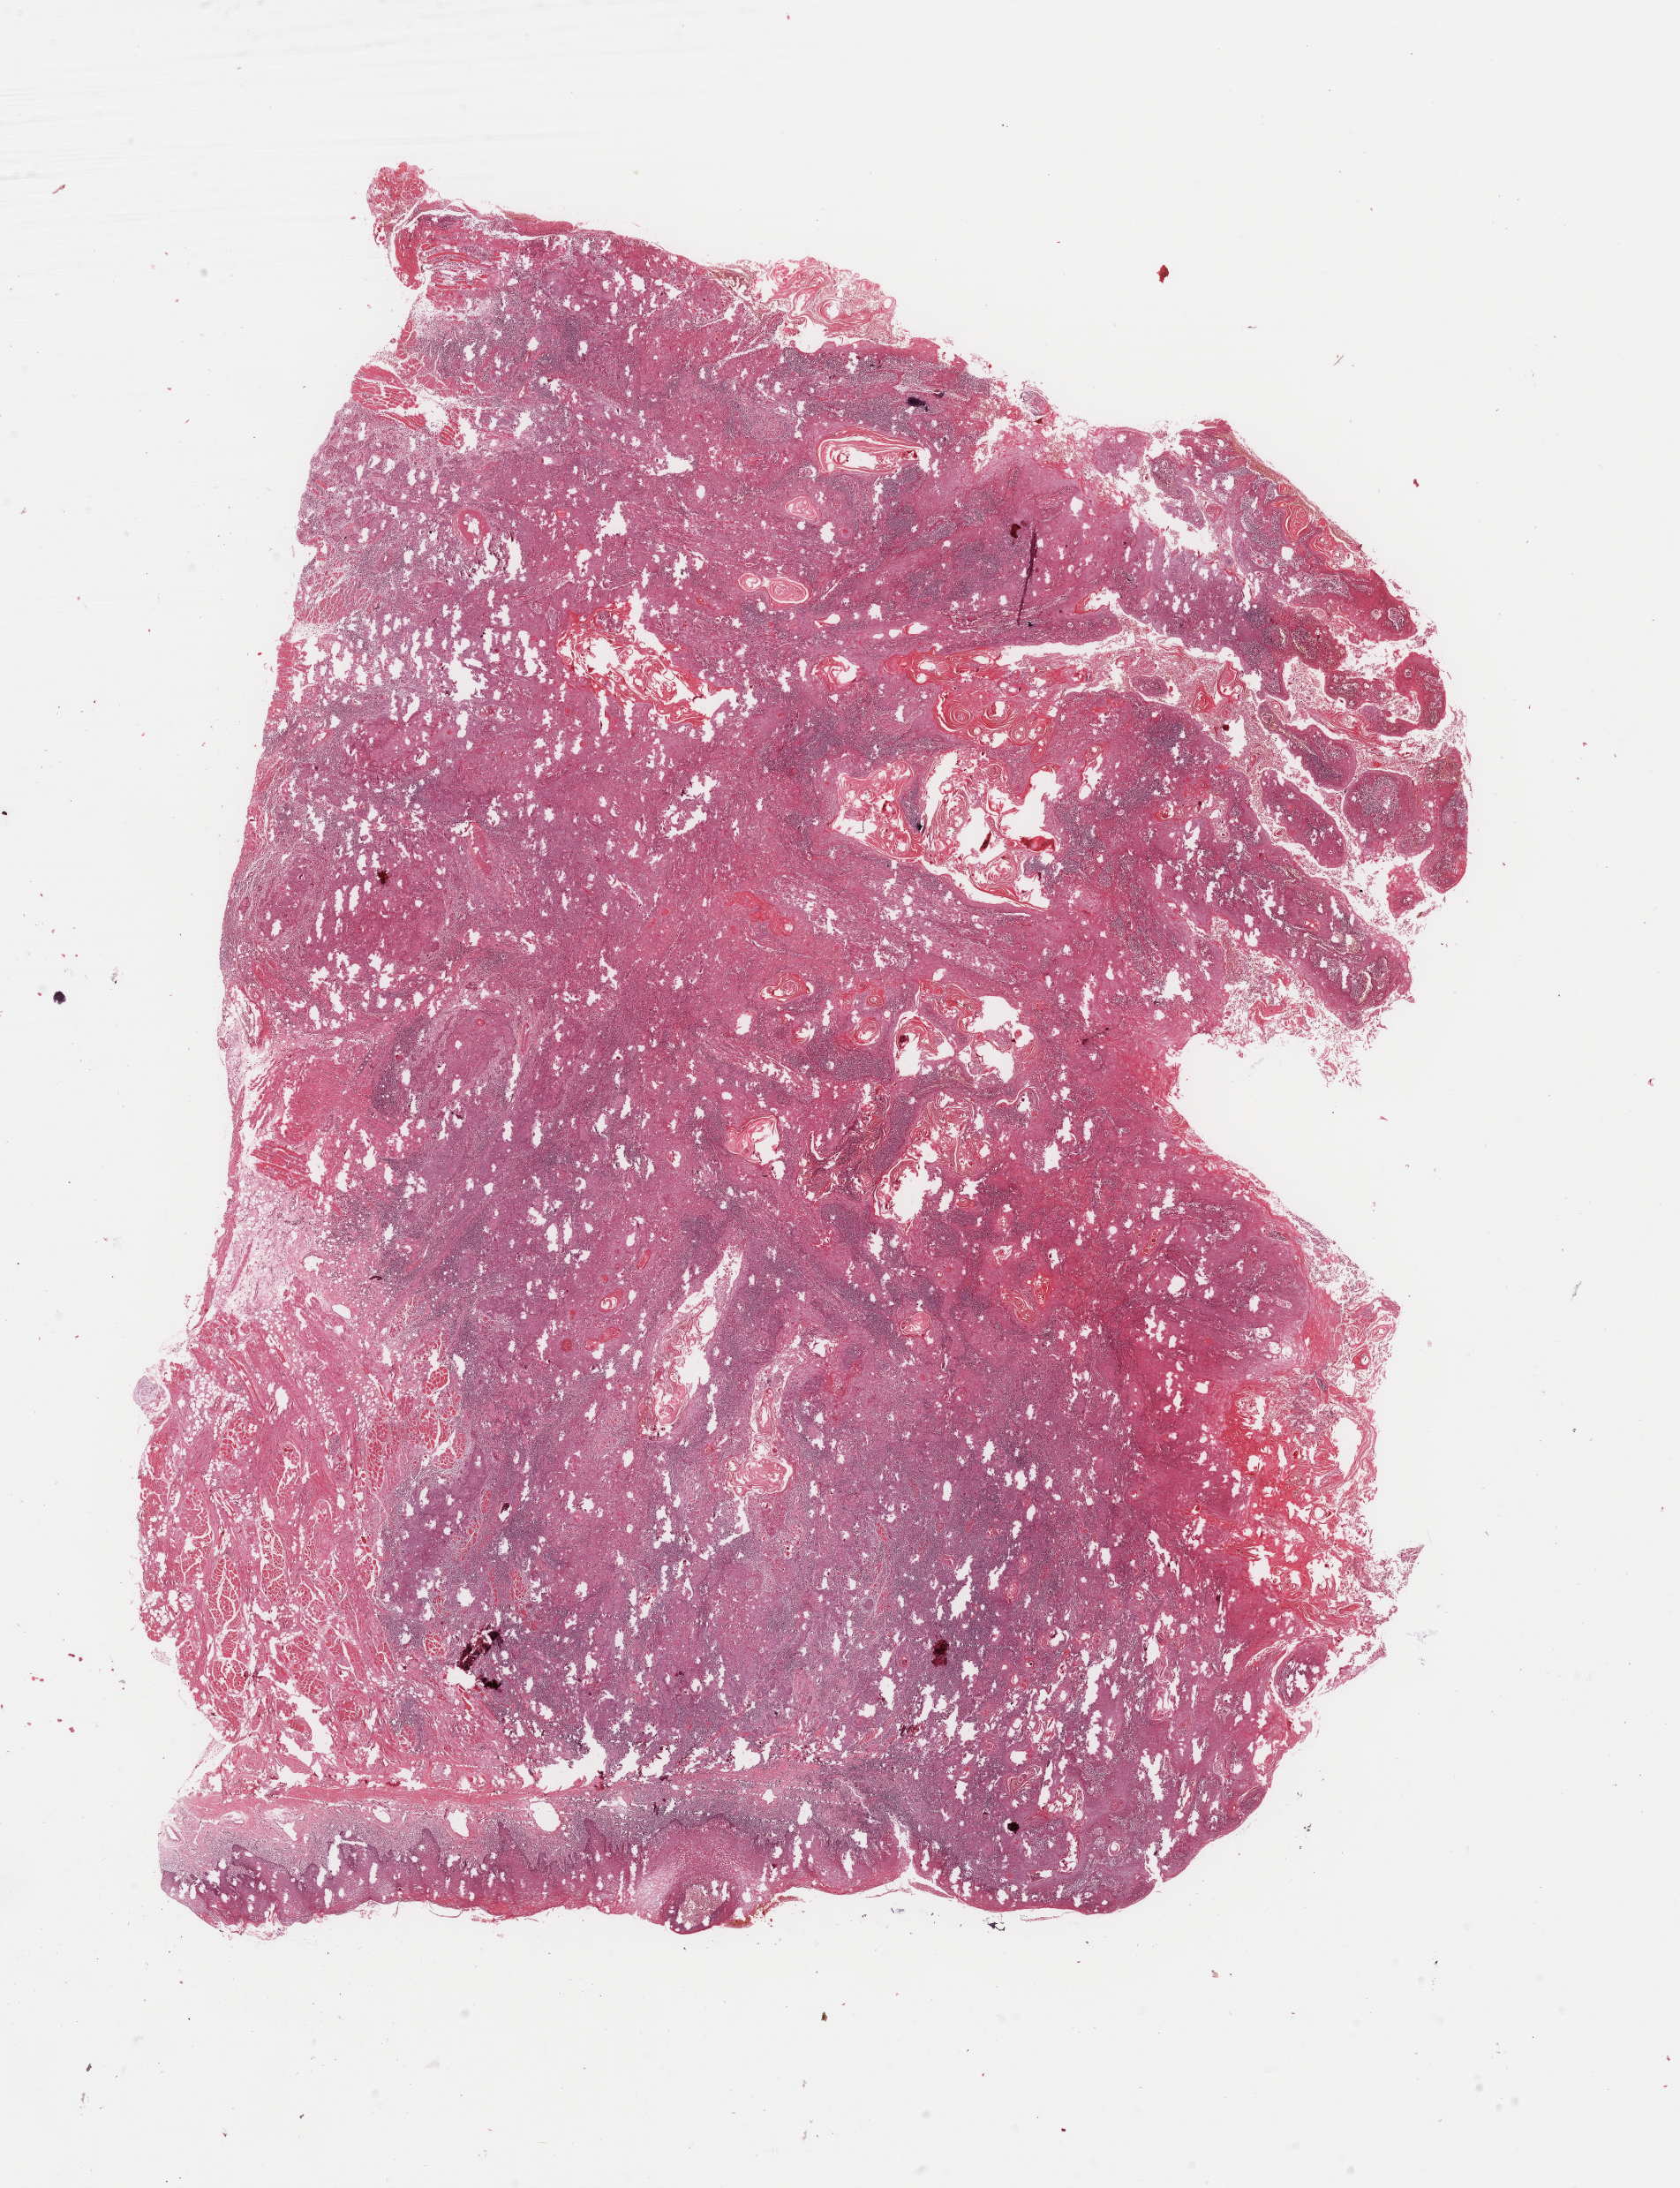
Digitized Hematoxylin and eosin (H&E) stained tissue section (whole slide), whole scanned area (about 15.1 x 19.7 mm, acquisition: 40x scan) shown as a low-resolution overview, formalin-fixed paraffin-embedded (FFPE) diagnostic section, sample: primary tumour, head and neck. Female patient; age at initial diagnosis 45 years. Histologic grade: G1 (well differentiated).
• AJCC pathologic stage: III (7th edition)
• diagnosis: Squamous cell carcinoma, NOS (tongue, NOS)